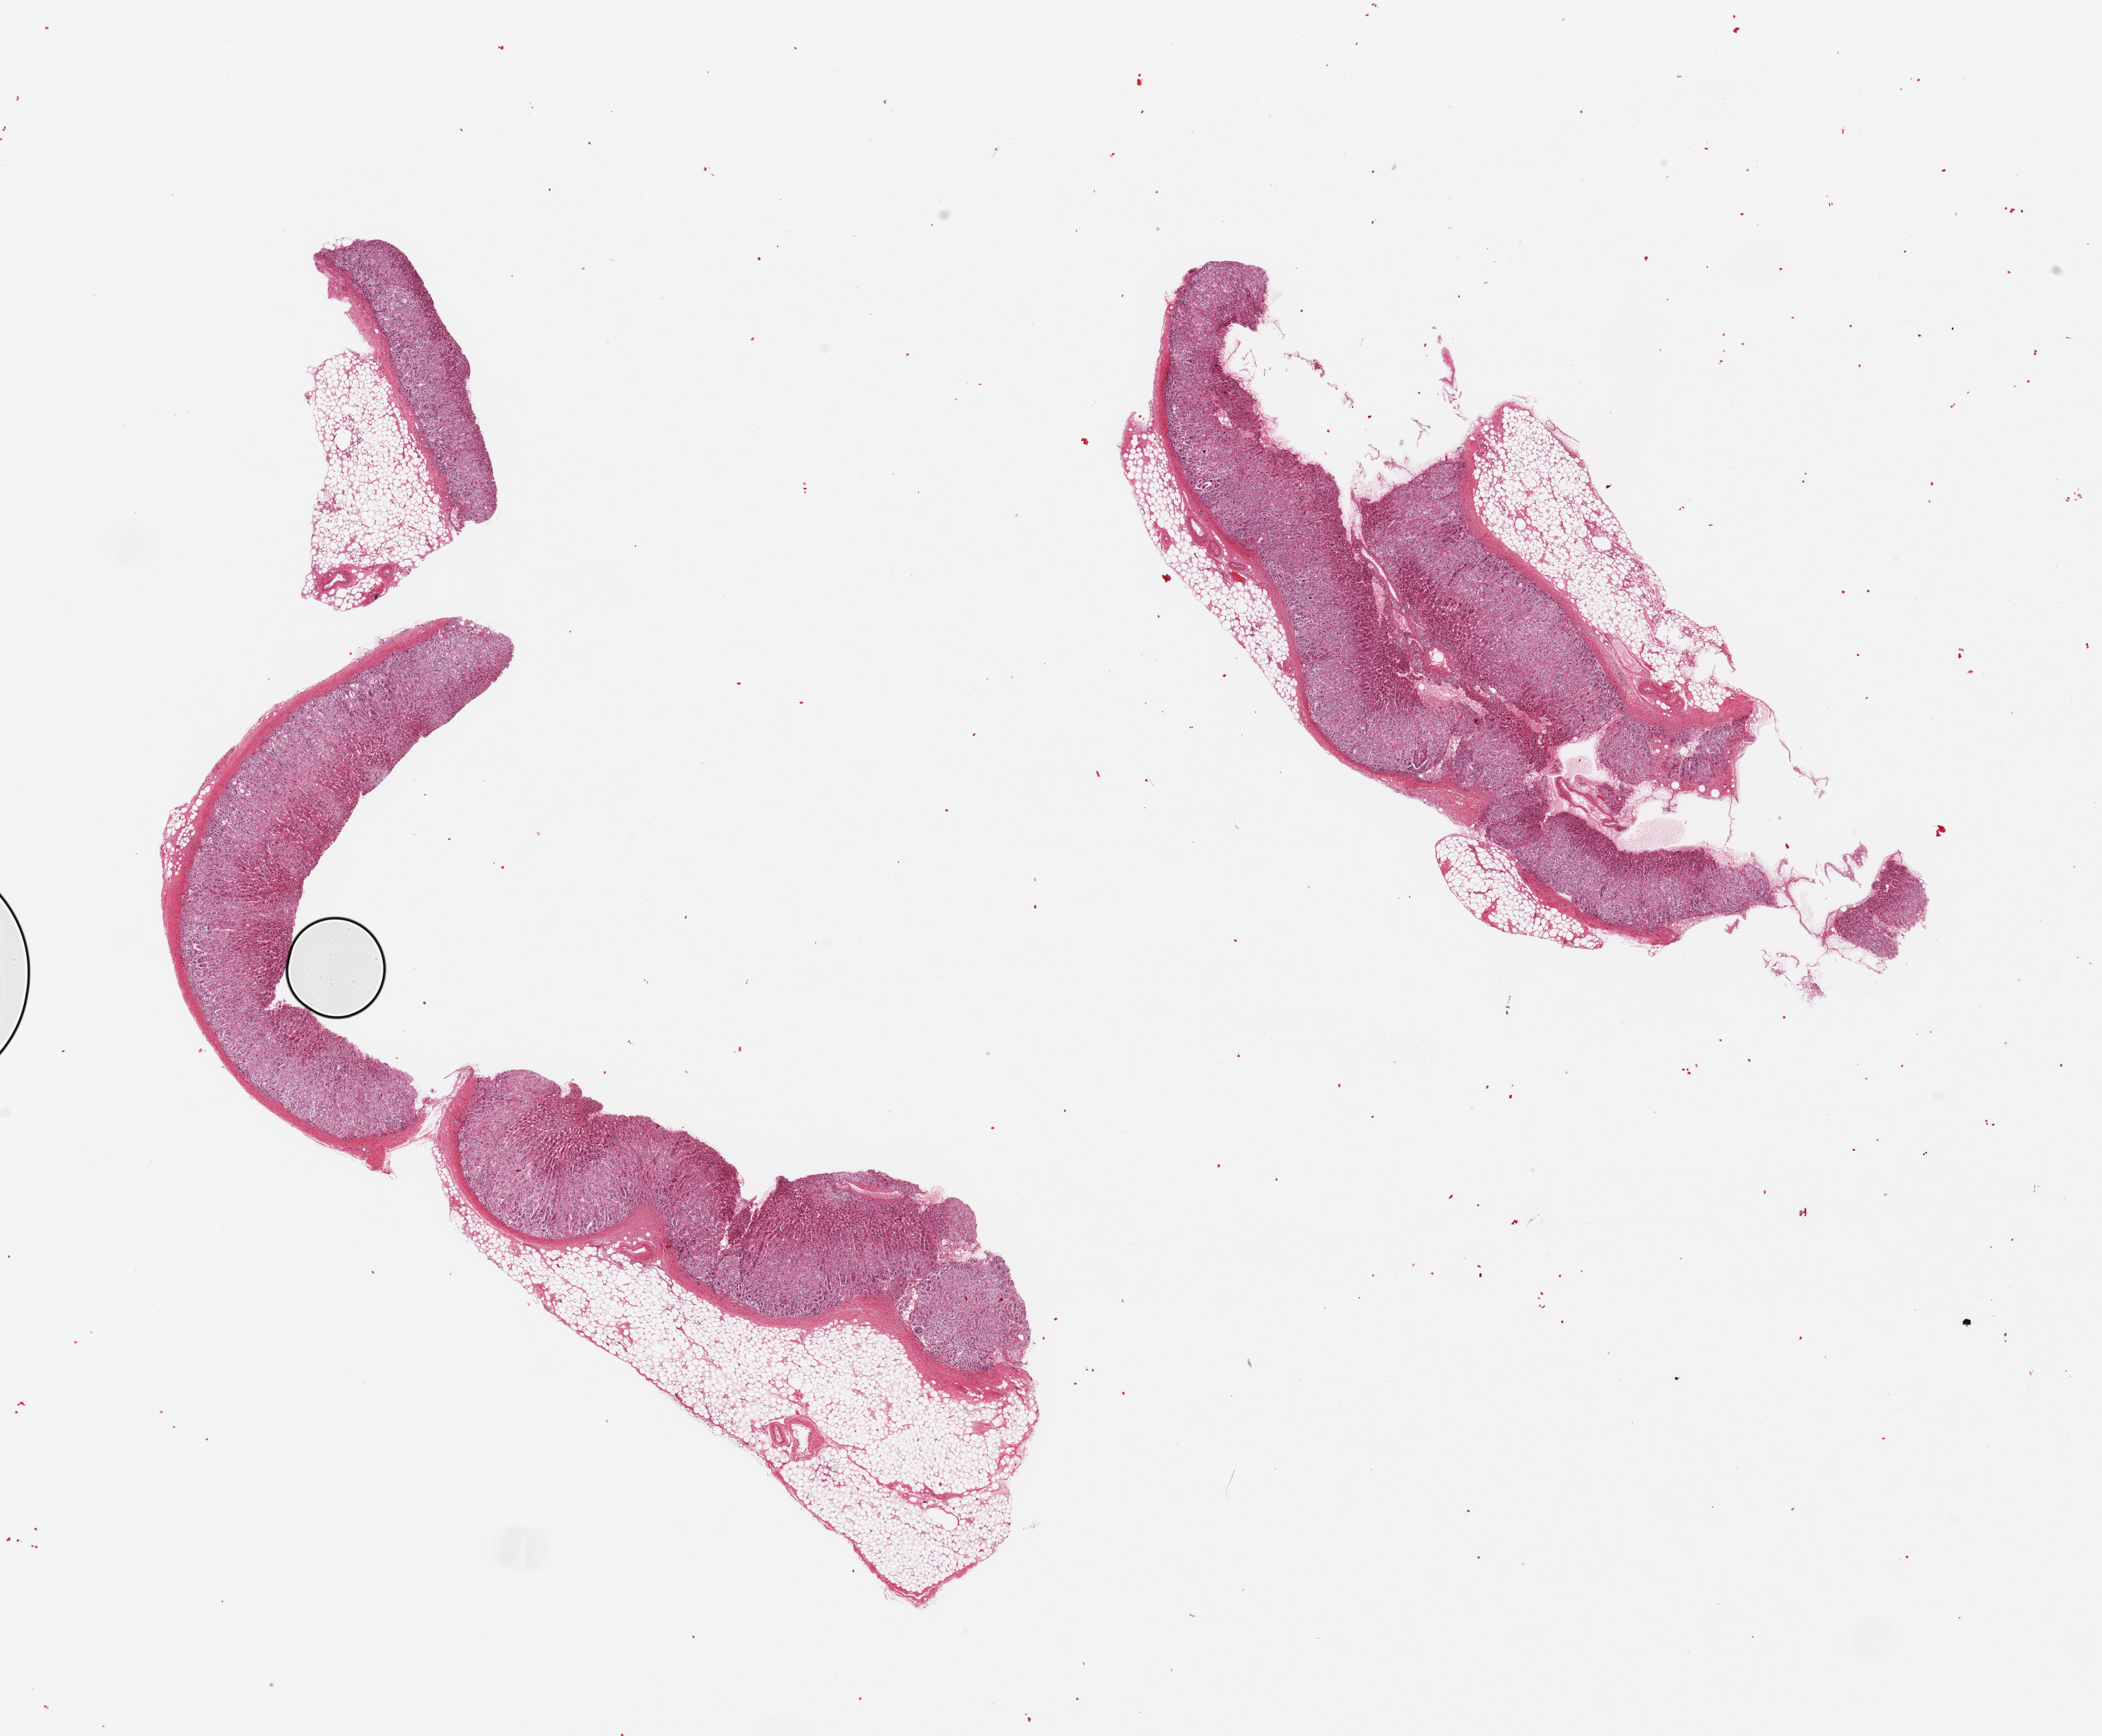
Haematoxylin and eosin whole-slide image, a low-resolution overview of the entire scanned area, about 23.6 x 19.5 mm; PAXgene-fixed paraffin-embedded (PFPE) section; sampled site (target tissue): adrenal gland; tissue donor sample. Donor sex: male.
Reviewer comment on this tissue sample: 2 pieces, all cortex, ~40% adherent fat.